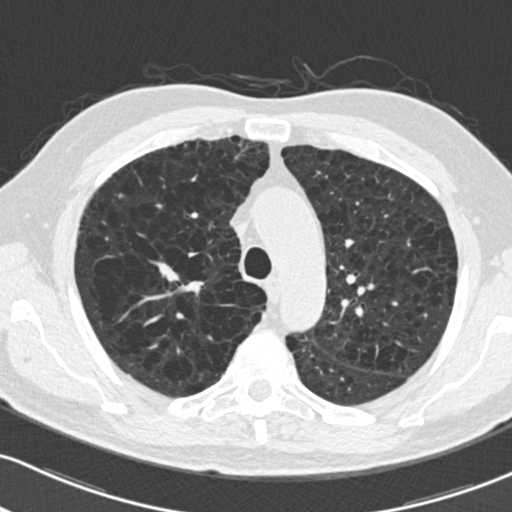
Axial slice from a low-dose chest CT screening exam. Second annual screen. Lung window (W 1500 / L -600 HU). Slice 53 of 204 in the series. Male, age 73 years at enrolment.
- Expert reader's lesion annotation, bounding box (x1, y1, x2, y2) in pixels: (149, 257, 197, 291).
- Reader record for this screening exam (exam-level; its link to the box is not recorded): non-calcified nodule or mass ≥4 mm, right upper lobe, 10 × 9 mm, smooth margins, soft tissue attenuation, pre-existing on the prior screen: yes; interval growth: yes.
- Later outcome: lung cancer diagnosed 51 days after this screen — squamous cell carcinoma, NOS, right upper lobe, stage IA (AJCC 6th edition), 10 mm at pathology.